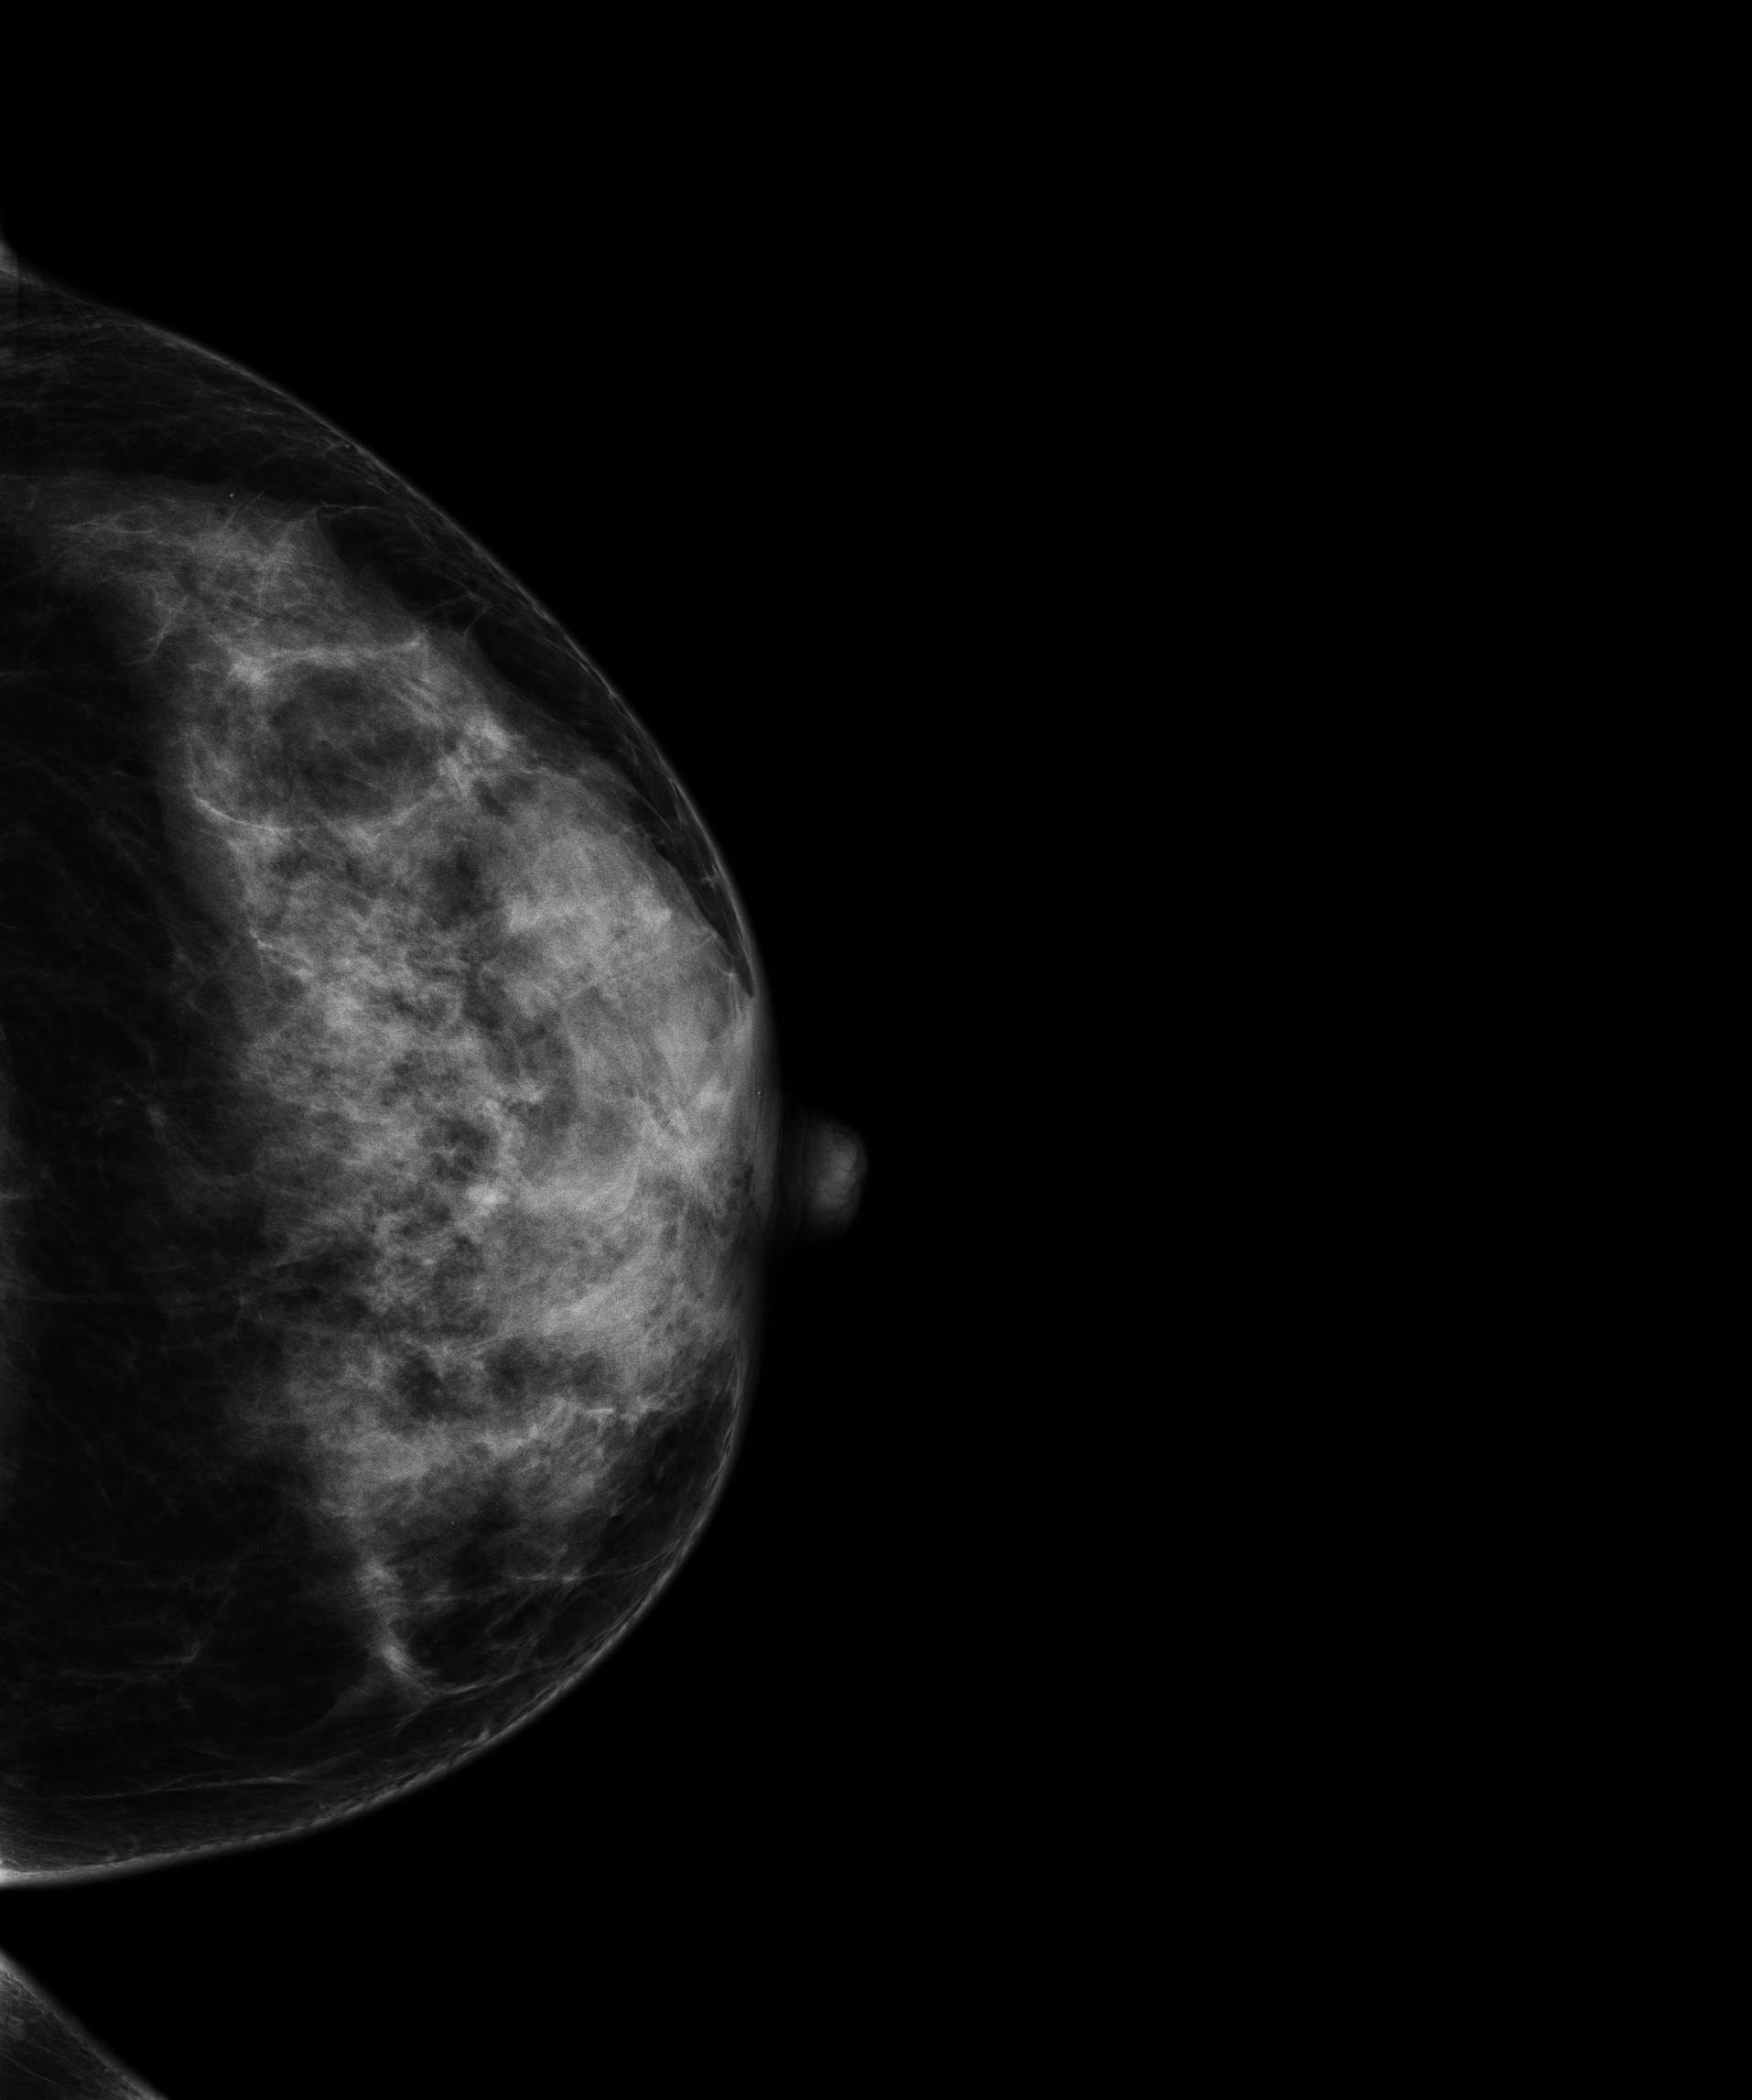
Digital mammogram (FFDM), left breast, craniocaudal (CC) view, annual screening mammography examination, system: Senographe Essential ADS_56.21.3. Patient: female, 56 years.
Breast density at the screening exam (both breasts): extremely dense (BI-RADS density category d). Final BI-RADS category for the screening round (tomosynthesis exam, both breasts): category 1. Recall: no recall after this screen.